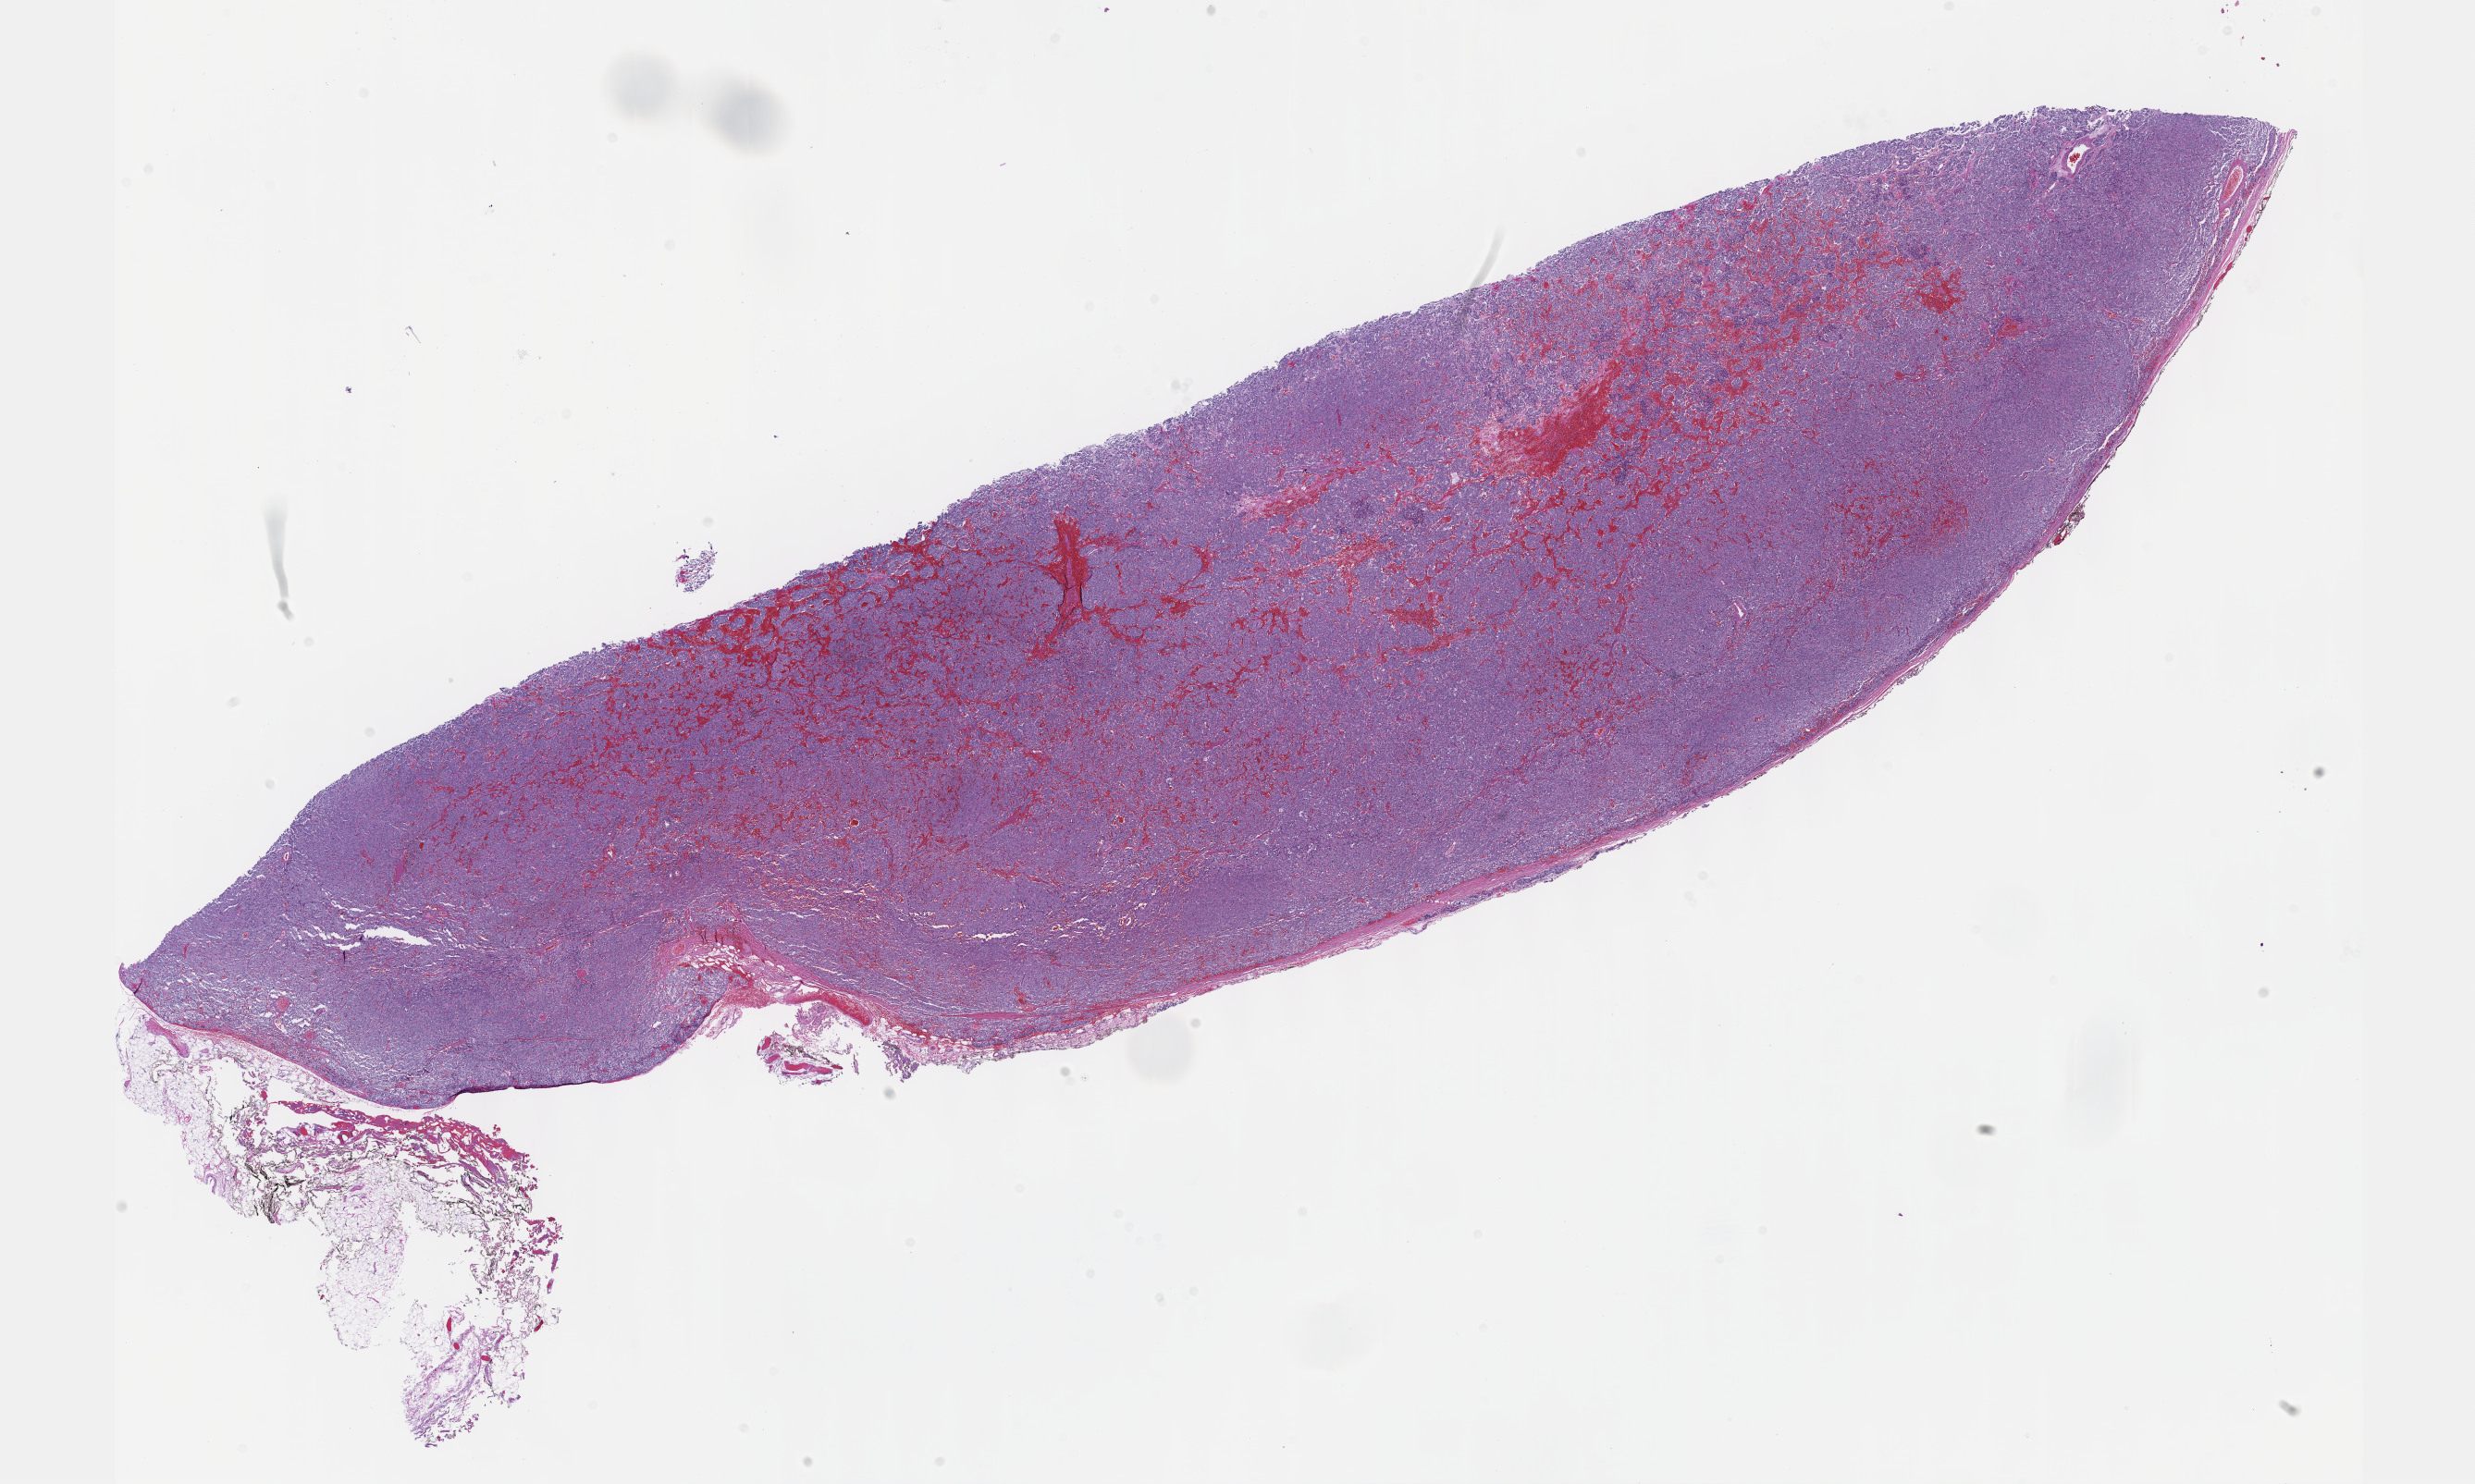
H&E whole-slide image, low-resolution overview of the scanned area, about 21.6 x 13.0 mm (slide scanned at 40x); formalin-fixed paraffin-embedded (FFPE) diagnostic section; primary tumour sample from the retroperitoneum and peritoneum. Female, age 40 years at initial diagnosis.
Diagnosis: Extra-adrenal paraganglioma, NOS (retroperitoneum). Lymph nodes positive (case pathology): 0 of 1 examined.